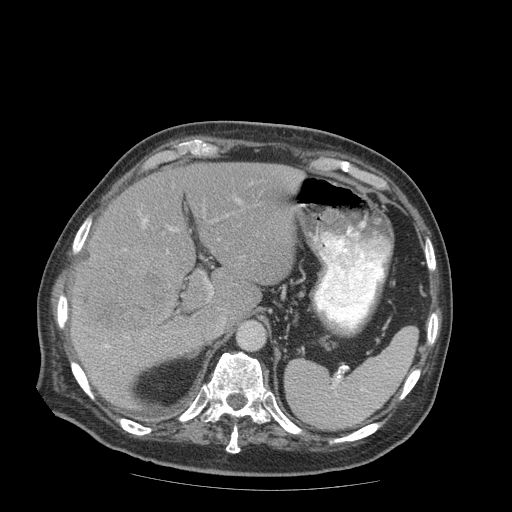
Contrast-enhanced abdominal CT (liver protocol), one axial slice; slice 57 of 99 in the series (ordered by position); 140 kVp; soft-tissue window (W 400 / L 40 HU); 2.5 mm slice thickness; 512 × 512 image matrix, field of view 420 × 420 mm. Case-level facts recorded for this patient, not image findings: diagnosis: hepatocellular carcinoma (patient treated with transarterial chemoembolisation; whether this scan precedes or follows treatment is not stated here); TNM stage (as recorded): Stage-IIIB; Child-Pugh class: A.
Outlined on this slice (semi-automatic segmentation, software-assisted and operator-edited):
- liver parenchyma outside the tumour (the mass and vessels are separate outlines, so this box may not span the whole liver): box from (x=70, y=162) to (x=304, y=410) px
- mass: (x=73, y=248)–(x=180, y=336)
- liver vessels: (x=105, y=199)–(x=240, y=348)